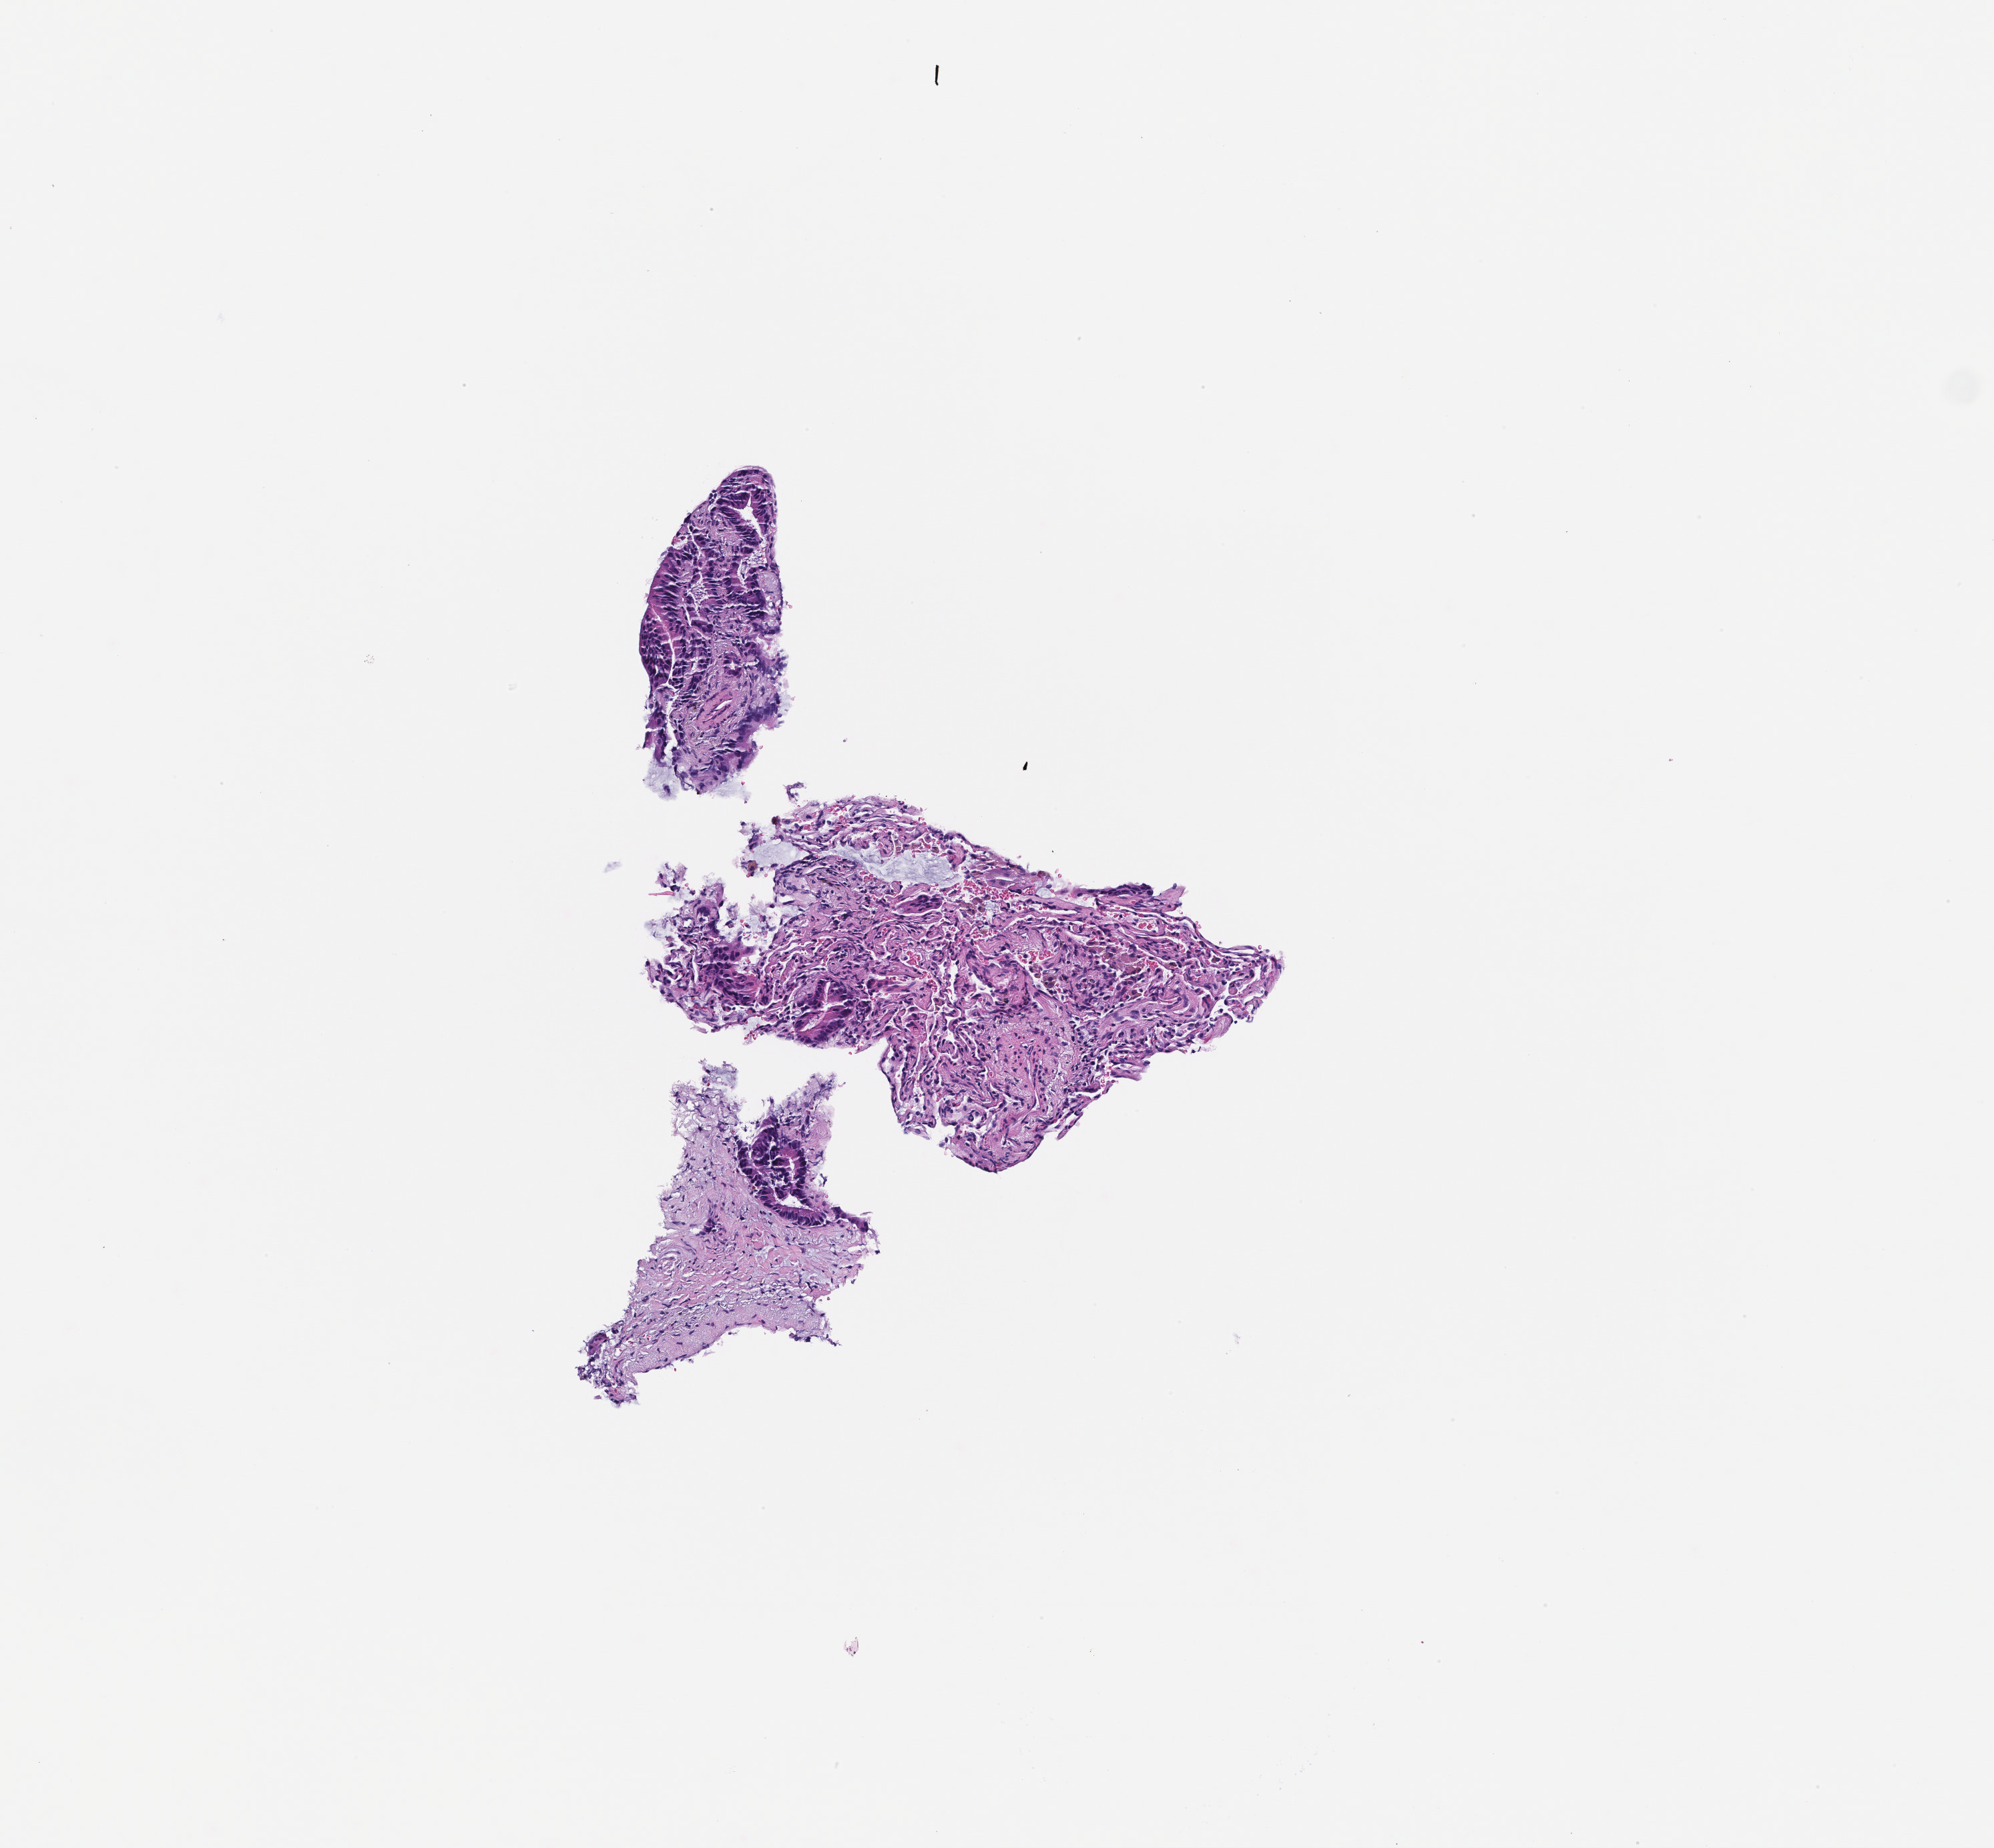
Hematoxylin and eosin (H&E) whole-slide image — shown as a low-resolution overview of the whole scanned area (about 3.0 x 2.8 mm); formalin-fixed, paraffin-embedded (FFPE) tissue; specimen time point: collected at disease progression. Patient sex: male.
* this section: metastatic tumor tissue
* primary diagnosis of the patient: Colorectal Carcinoma